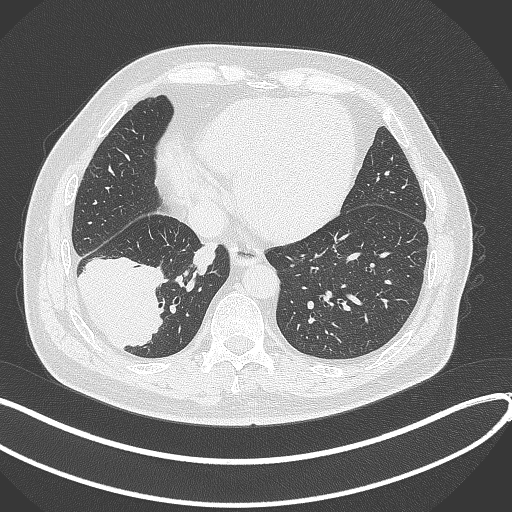
Chest CT, one axial slice. Position 103 of 360 along the scan axis. Reconstruction kernel B70f. 120 kVp. Lung window (W 1500 / L -600 HU). 1 mm slice thickness. 512 × 512 image matrix. Male patient, age 59 years.
Annotated regions visible in this slice (rectangle marked by the reading radiologist):
- lung tumour (recorded histology: adenocarcinoma): bounding box (x1, y1, x2, y2) in pixels: (78, 253, 167, 352)